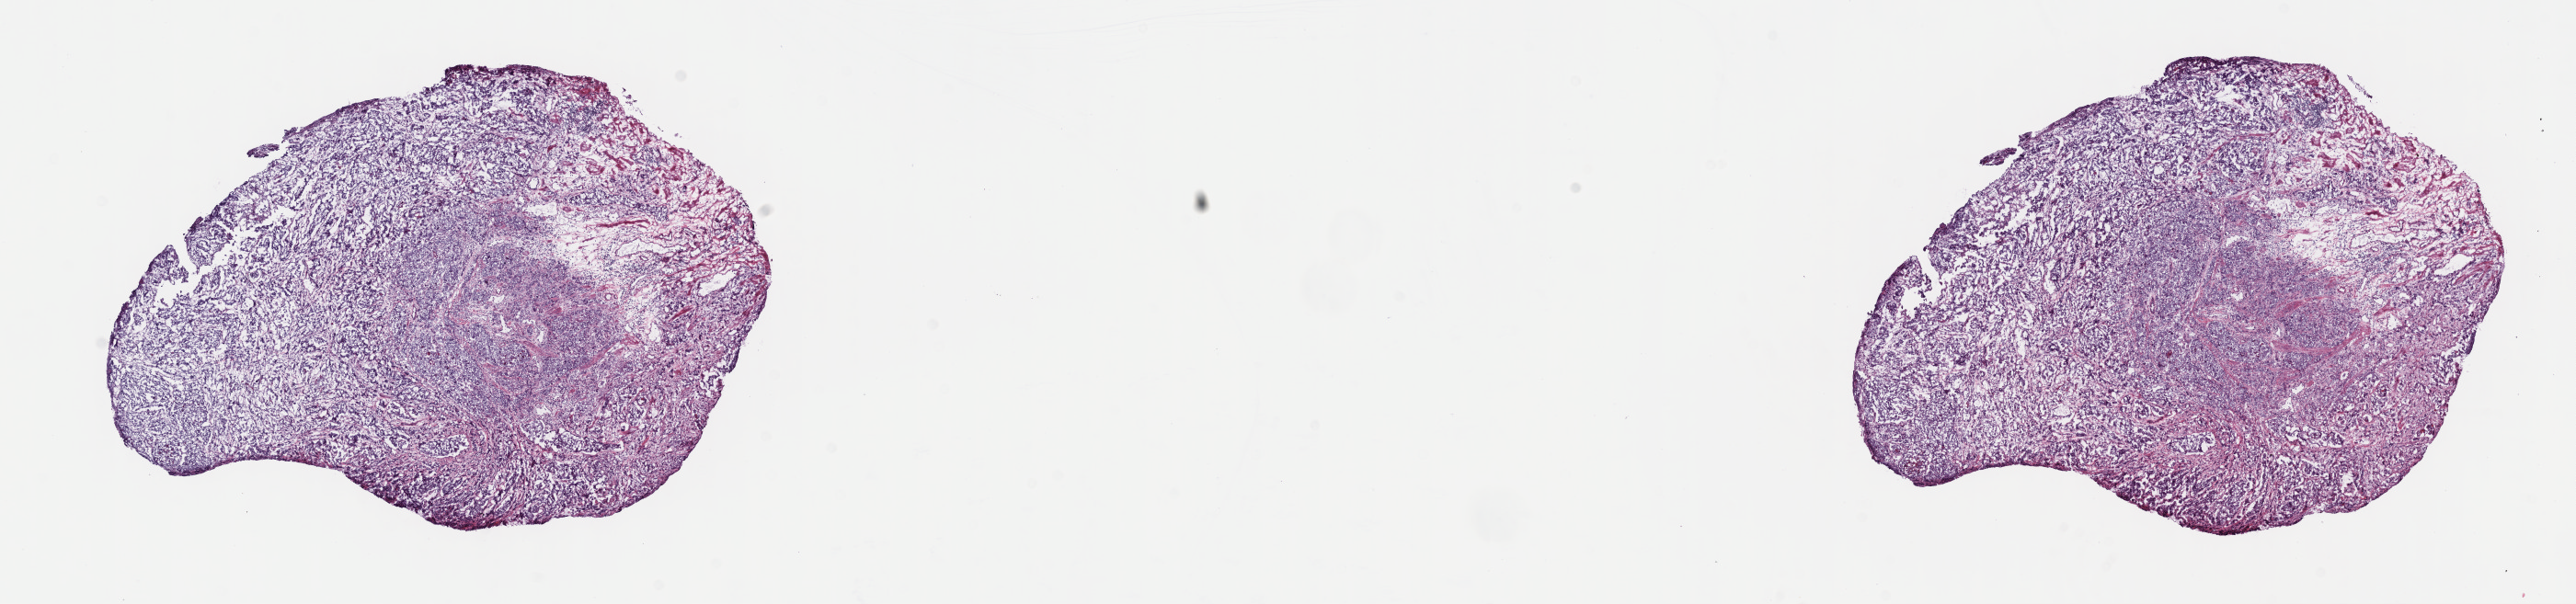
Whole-slide histology image, Hematoxylin and eosin (H&E) stained — low-resolution overview of the scanned area, about 22.7 x 5.3 mm (slide scanned at 40x); frozen section from the top of the tissue portion; primary tumour sample from the bladder. Female, age 67 years at initial diagnosis. Histologic grade: high grade. Pathologist review of this section (percent, as recorded): tumour cells 100%, tumour nuclei 80%, normal cells 0%, stromal cells 0%, necrosis 0%. Inflammatory infiltration, as recorded: lymphocyte infiltration 2%, monocyte infiltration 0%, neutrophil infiltration 0%.
* lymph nodes positive (case pathology): 0 of 16 examined
* pathologic diagnosis: Transitional cell carcinoma
* AJCC pathologic stage: III (7th edition)